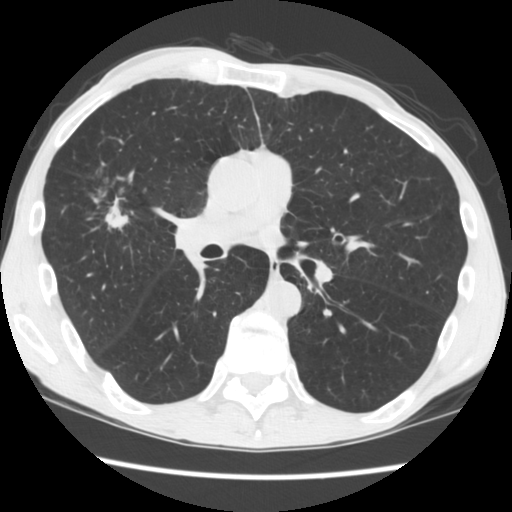
Low-dose screening chest CT, one axial slice; slice 95 of 181 in the series (ordered by position); reconstruction kernel STANDARD; 120 kVp; lung window (W 1500 / L -600 HU); 2.5 mm slice thickness; 512 × 512 image matrix, field of view 330 × 330 mm.
Structures marked on this image (expert manual segmentation):
- lesion 1 (tumor, upper lobe of right lung): bounding box <105,196,129,231> (left, top, right, bottom; pixels)